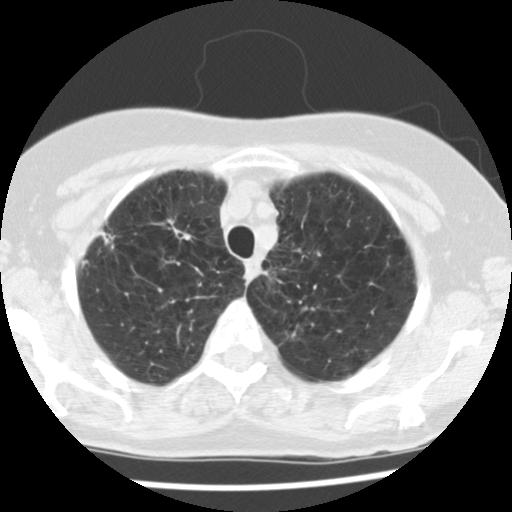
Low-dose screening chest CT, axial slice, first (baseline) screen, lung window (W 1500 / L -600 HU), 512 × 512 image matrix. Female participant, aged 70 years at enrolment. Former smoker at enrolment.
- Lesion marked by an expert reader, box from (x=151, y=207) to (x=213, y=256) px.
- Screening reader's record for this exam (one nodule recorded; not confirmed to be the boxed lesion): non-calcified nodule or mass ≥4 mm, left upper lobe, 8 × 6 mm, poorly defined margins, soft tissue attenuation.
- Note: the box lies in the patient's right hemithorax on this image, whereas the reader's record names the left lung; they may be different findings.
- Later outcome: lung cancer diagnosed 745 days after this screen — non-small cell carcinoma, right upper lobe, stage IV (AJCC 6th edition), 30 mm at pathology.